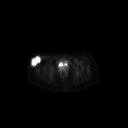
FDG PET of an extremity soft-tissue mass (from a PET/CT study), one axial slice; 128 × 128 image matrix, field of view 700 × 700 mm. Female patient, age 34 years. Case-level facts recorded for this patient, not image findings: histological type: synovial sarcoma; grade: intermediate; site of the primary tumour: right thigh.
Annotated regions visible in this slice (expert contour drawn on MRI and transferred to this co-registered scan by the dataset authors):
- gross tumour volume including surrounding oedema: bounding box <30,56,41,67> (left, top, right, bottom; pixels)
- gross tumour volume (mass): <30,56,41,67>